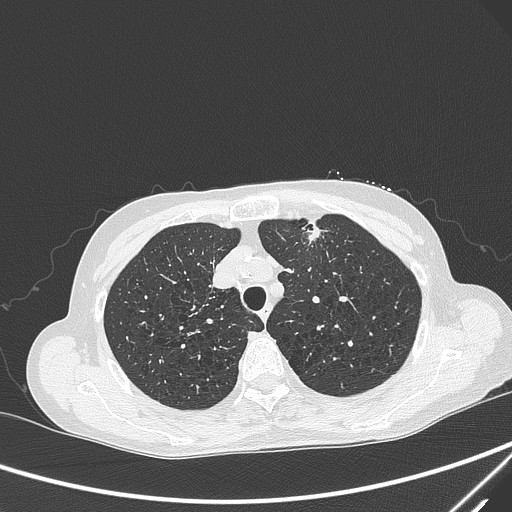
Chest CT, one axial slice. Position 235 of 299 along the scan axis. Lung window (W 1500 / L -600 HU). 1 mm slice thickness. 512 × 512 image matrix. Female patient, age 71 years. From the clinical record (not read from this slice): clinical TNM (as recorded): T1c N0 M0; histopathological grade: G2-3.
Structures marked on this image (rectangle marked by the reading radiologist):
- lung tumour (recorded histology: adenocarcinoma): bounding box [x1, y1, x2, y2] px = [297, 215, 328, 253]